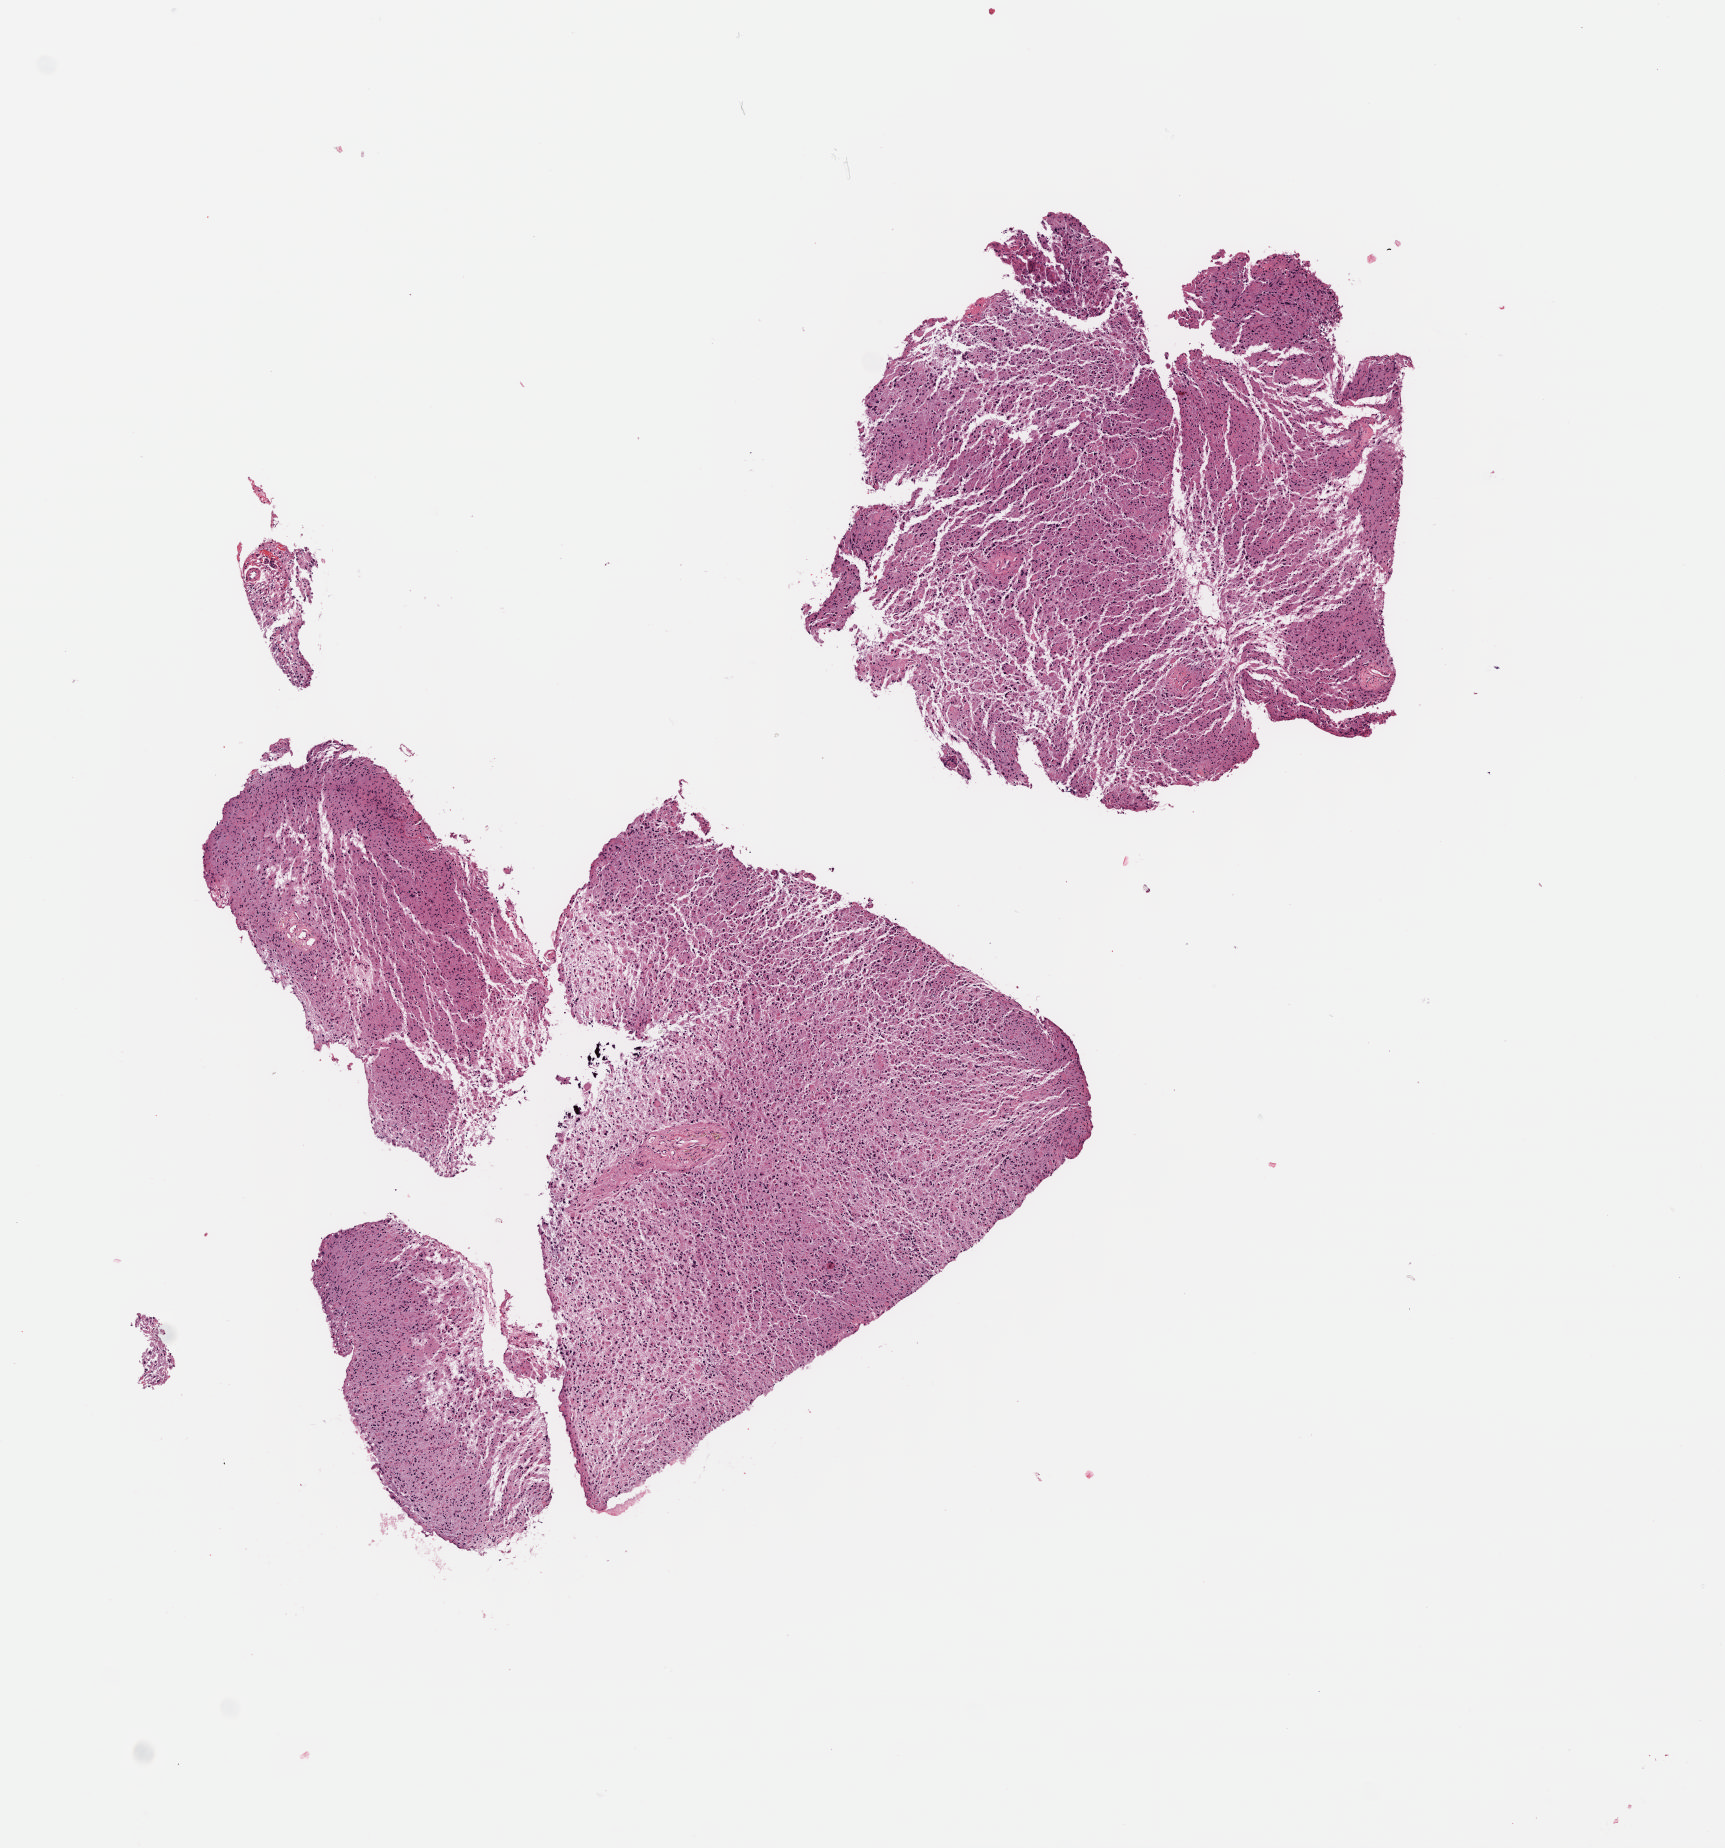
Digitized H&E-stained tissue section (whole slide), low-resolution overview of the scanned area, about 6.8 x 7.3 mm, formalin-fixed paraffin-embedded (FFPE) diagnostic section, primary tumour sample from the brain. Male, age 36 years at initial diagnosis. Histologic grade: G2 (moderately differentiated).
Diagnosis: Astrocytoma, NOS (cerebrum).